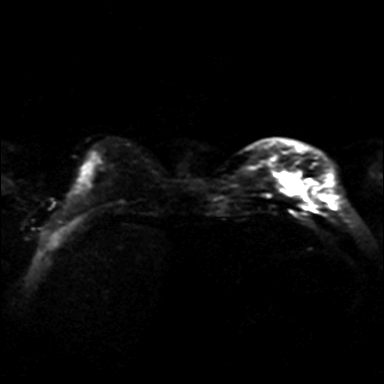
Breast MRI, one axial slice; slice 8 of 36 in the series (ordered by position); diffusion-weighted series; image 2 of 4 stored at this slice position (different b-values; order by instance number); 3 T; 4 mm slice thickness; 384 × 384 image matrix, field of view 320 × 320 mm. Female patient.
Outlined on this slice (manually delineated by an expert):
- tumour on diffusion-weighted imaging: bounding box (x1, y1, x2, y2) in pixels: (280, 171, 300, 193)